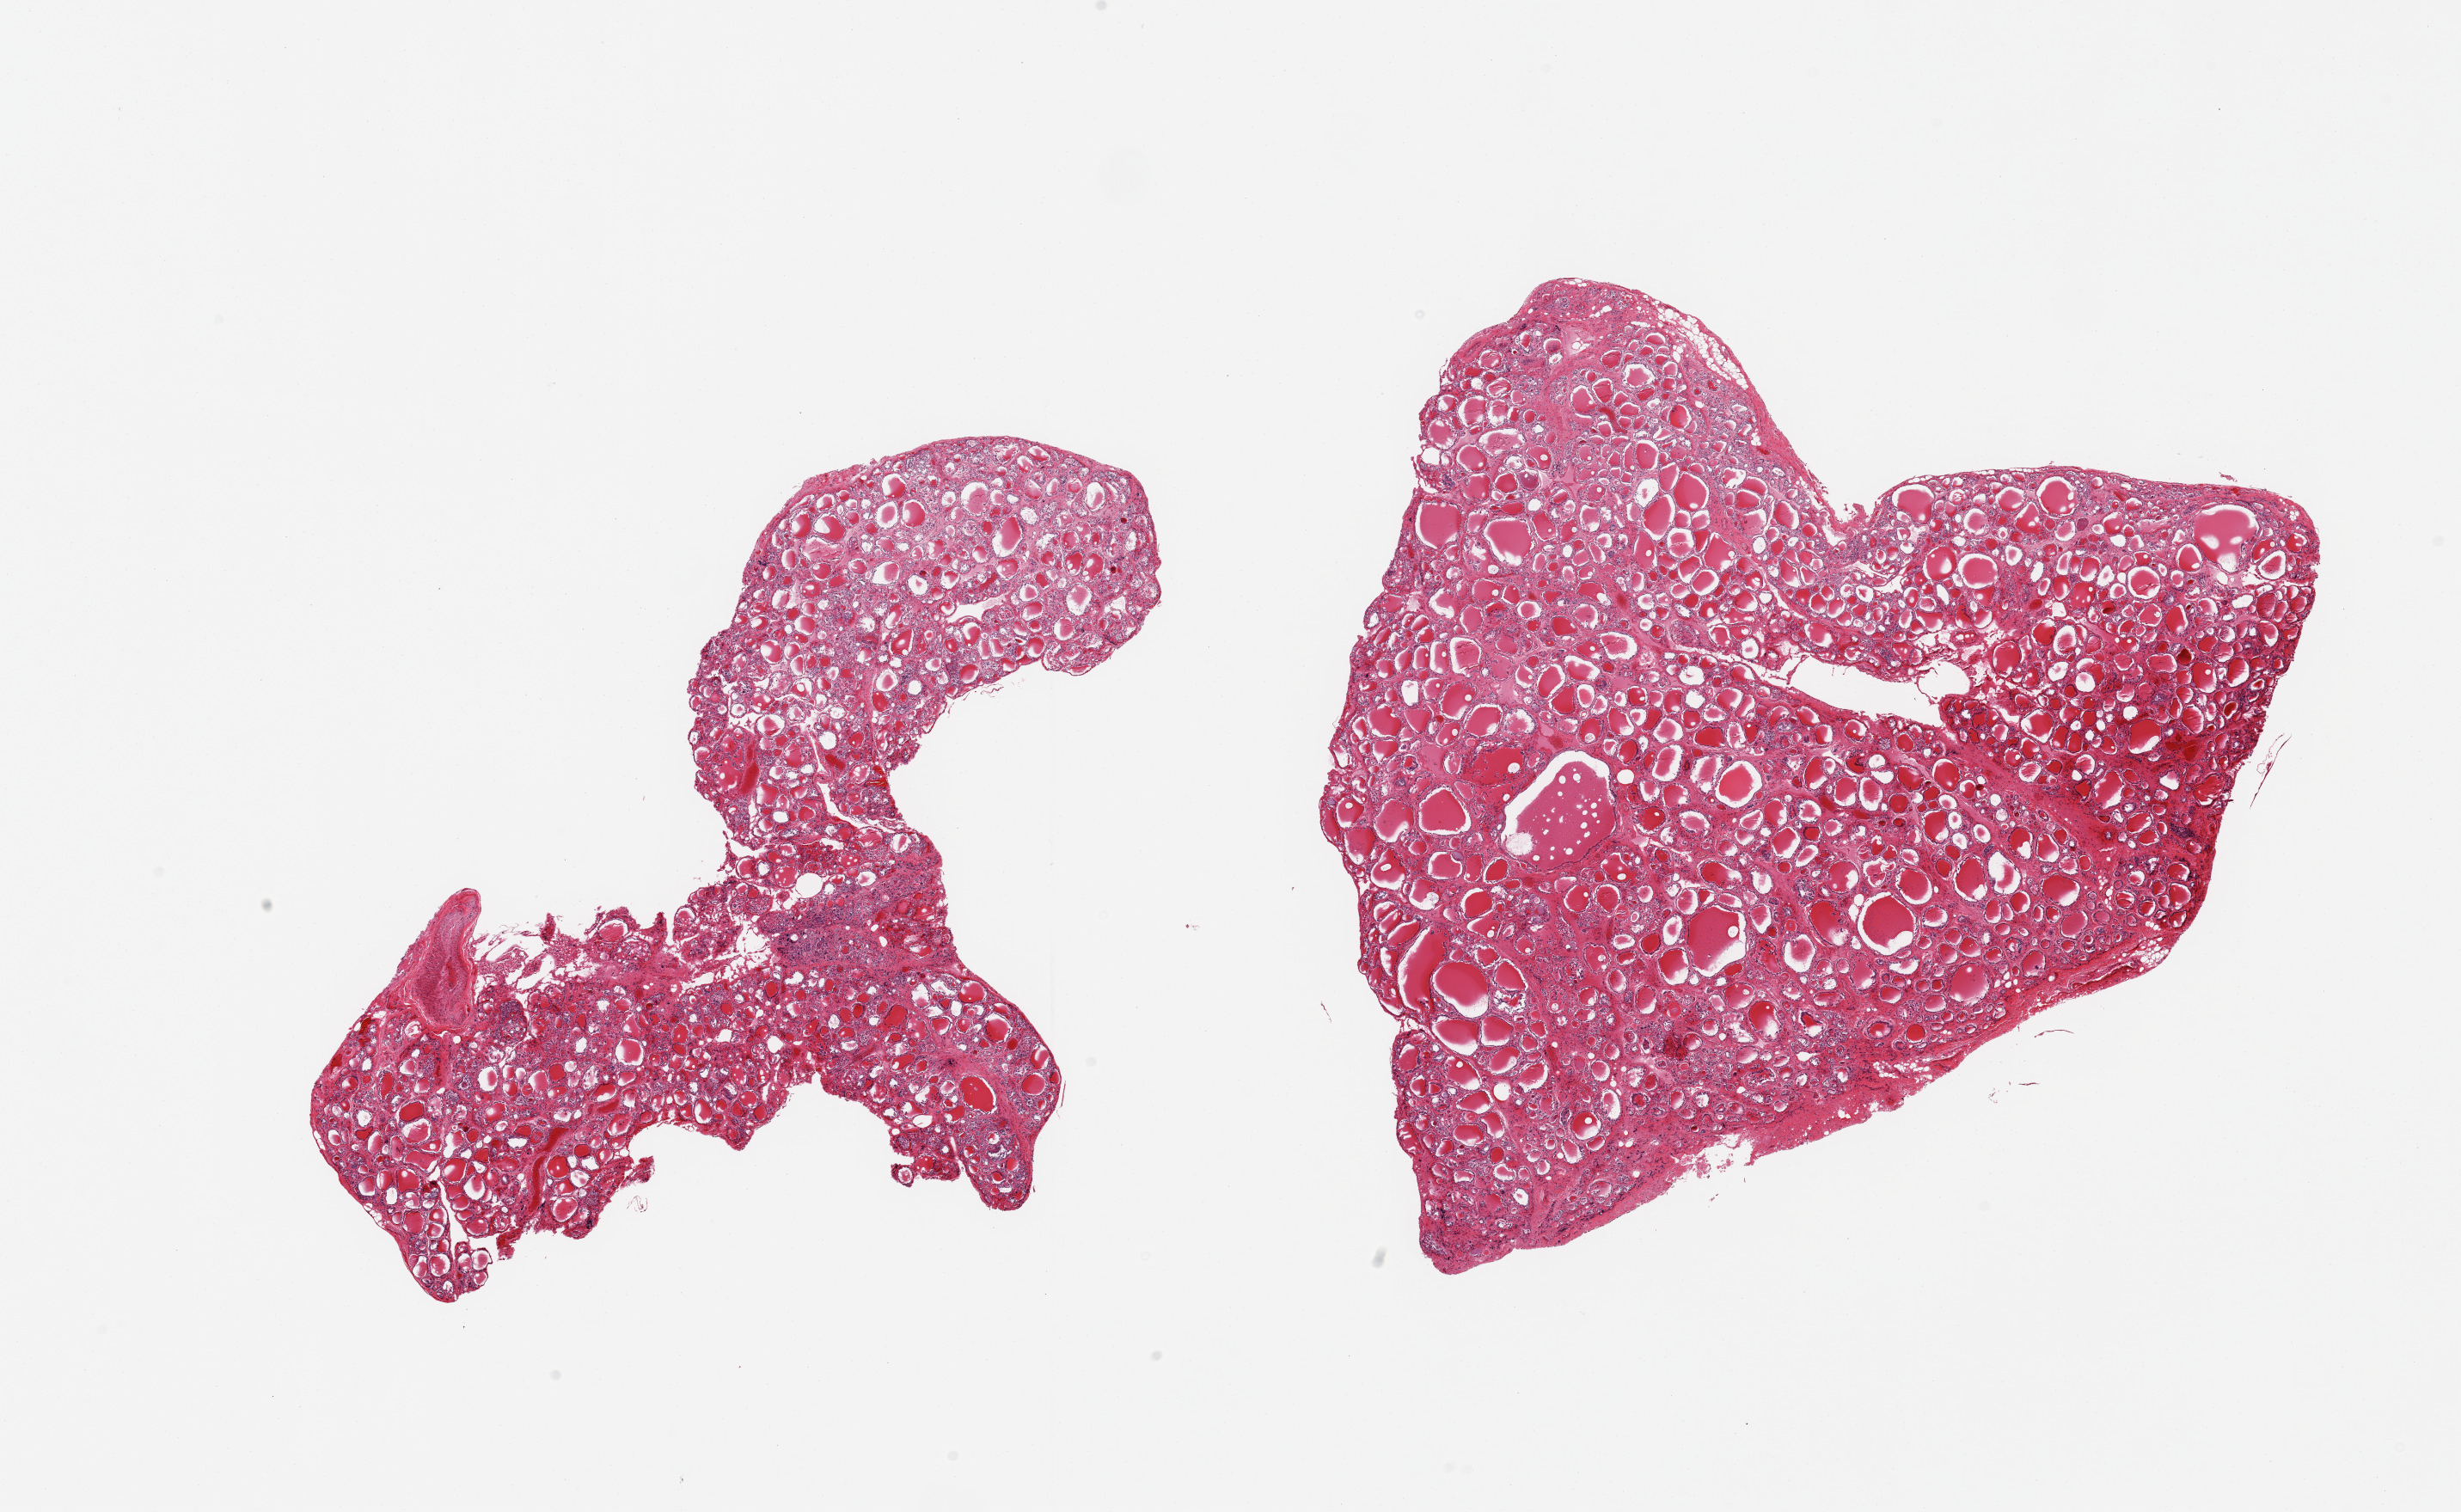
Hematoxylin and eosin (H&E) whole-slide image, brightfield — whole scanned area (about 22.6 x 13.9 mm) shown as a low-resolution overview. PAXgene-fixed, paraffin-embedded tissue. Section of thyroid (target tissue). Donor tissue sample. Male donor.
Review note (as recorded): 2 pieces, no abnormalities; small colloid cyst (~1mm).